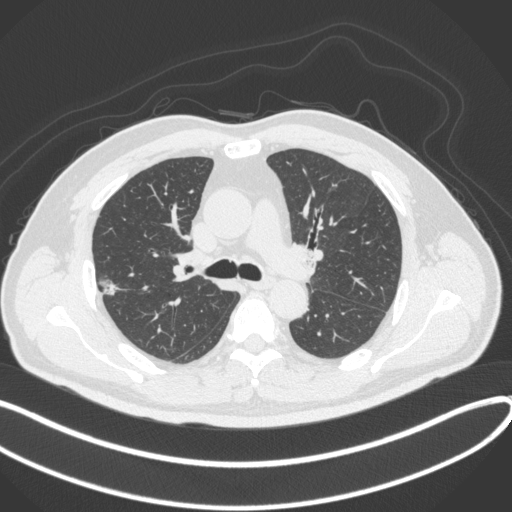
Chest CT, one axial slice; position 221 of 373 along the scan axis; reconstruction kernel B31f; 120 kVp; lung window (W 1500 / L -600 HU); 1 mm slice thickness; 512 × 512 image matrix, field of view 400 × 400 mm. Male patient, age 60 years. From the clinical record (not read from this slice): clinical TNM (as recorded): T1c N0 M0.
Structures marked on this image (rectangle marked by the reading radiologist):
- lung tumour (recorded histology: adenocarcinoma): box from (x=97, y=271) to (x=129, y=298) px